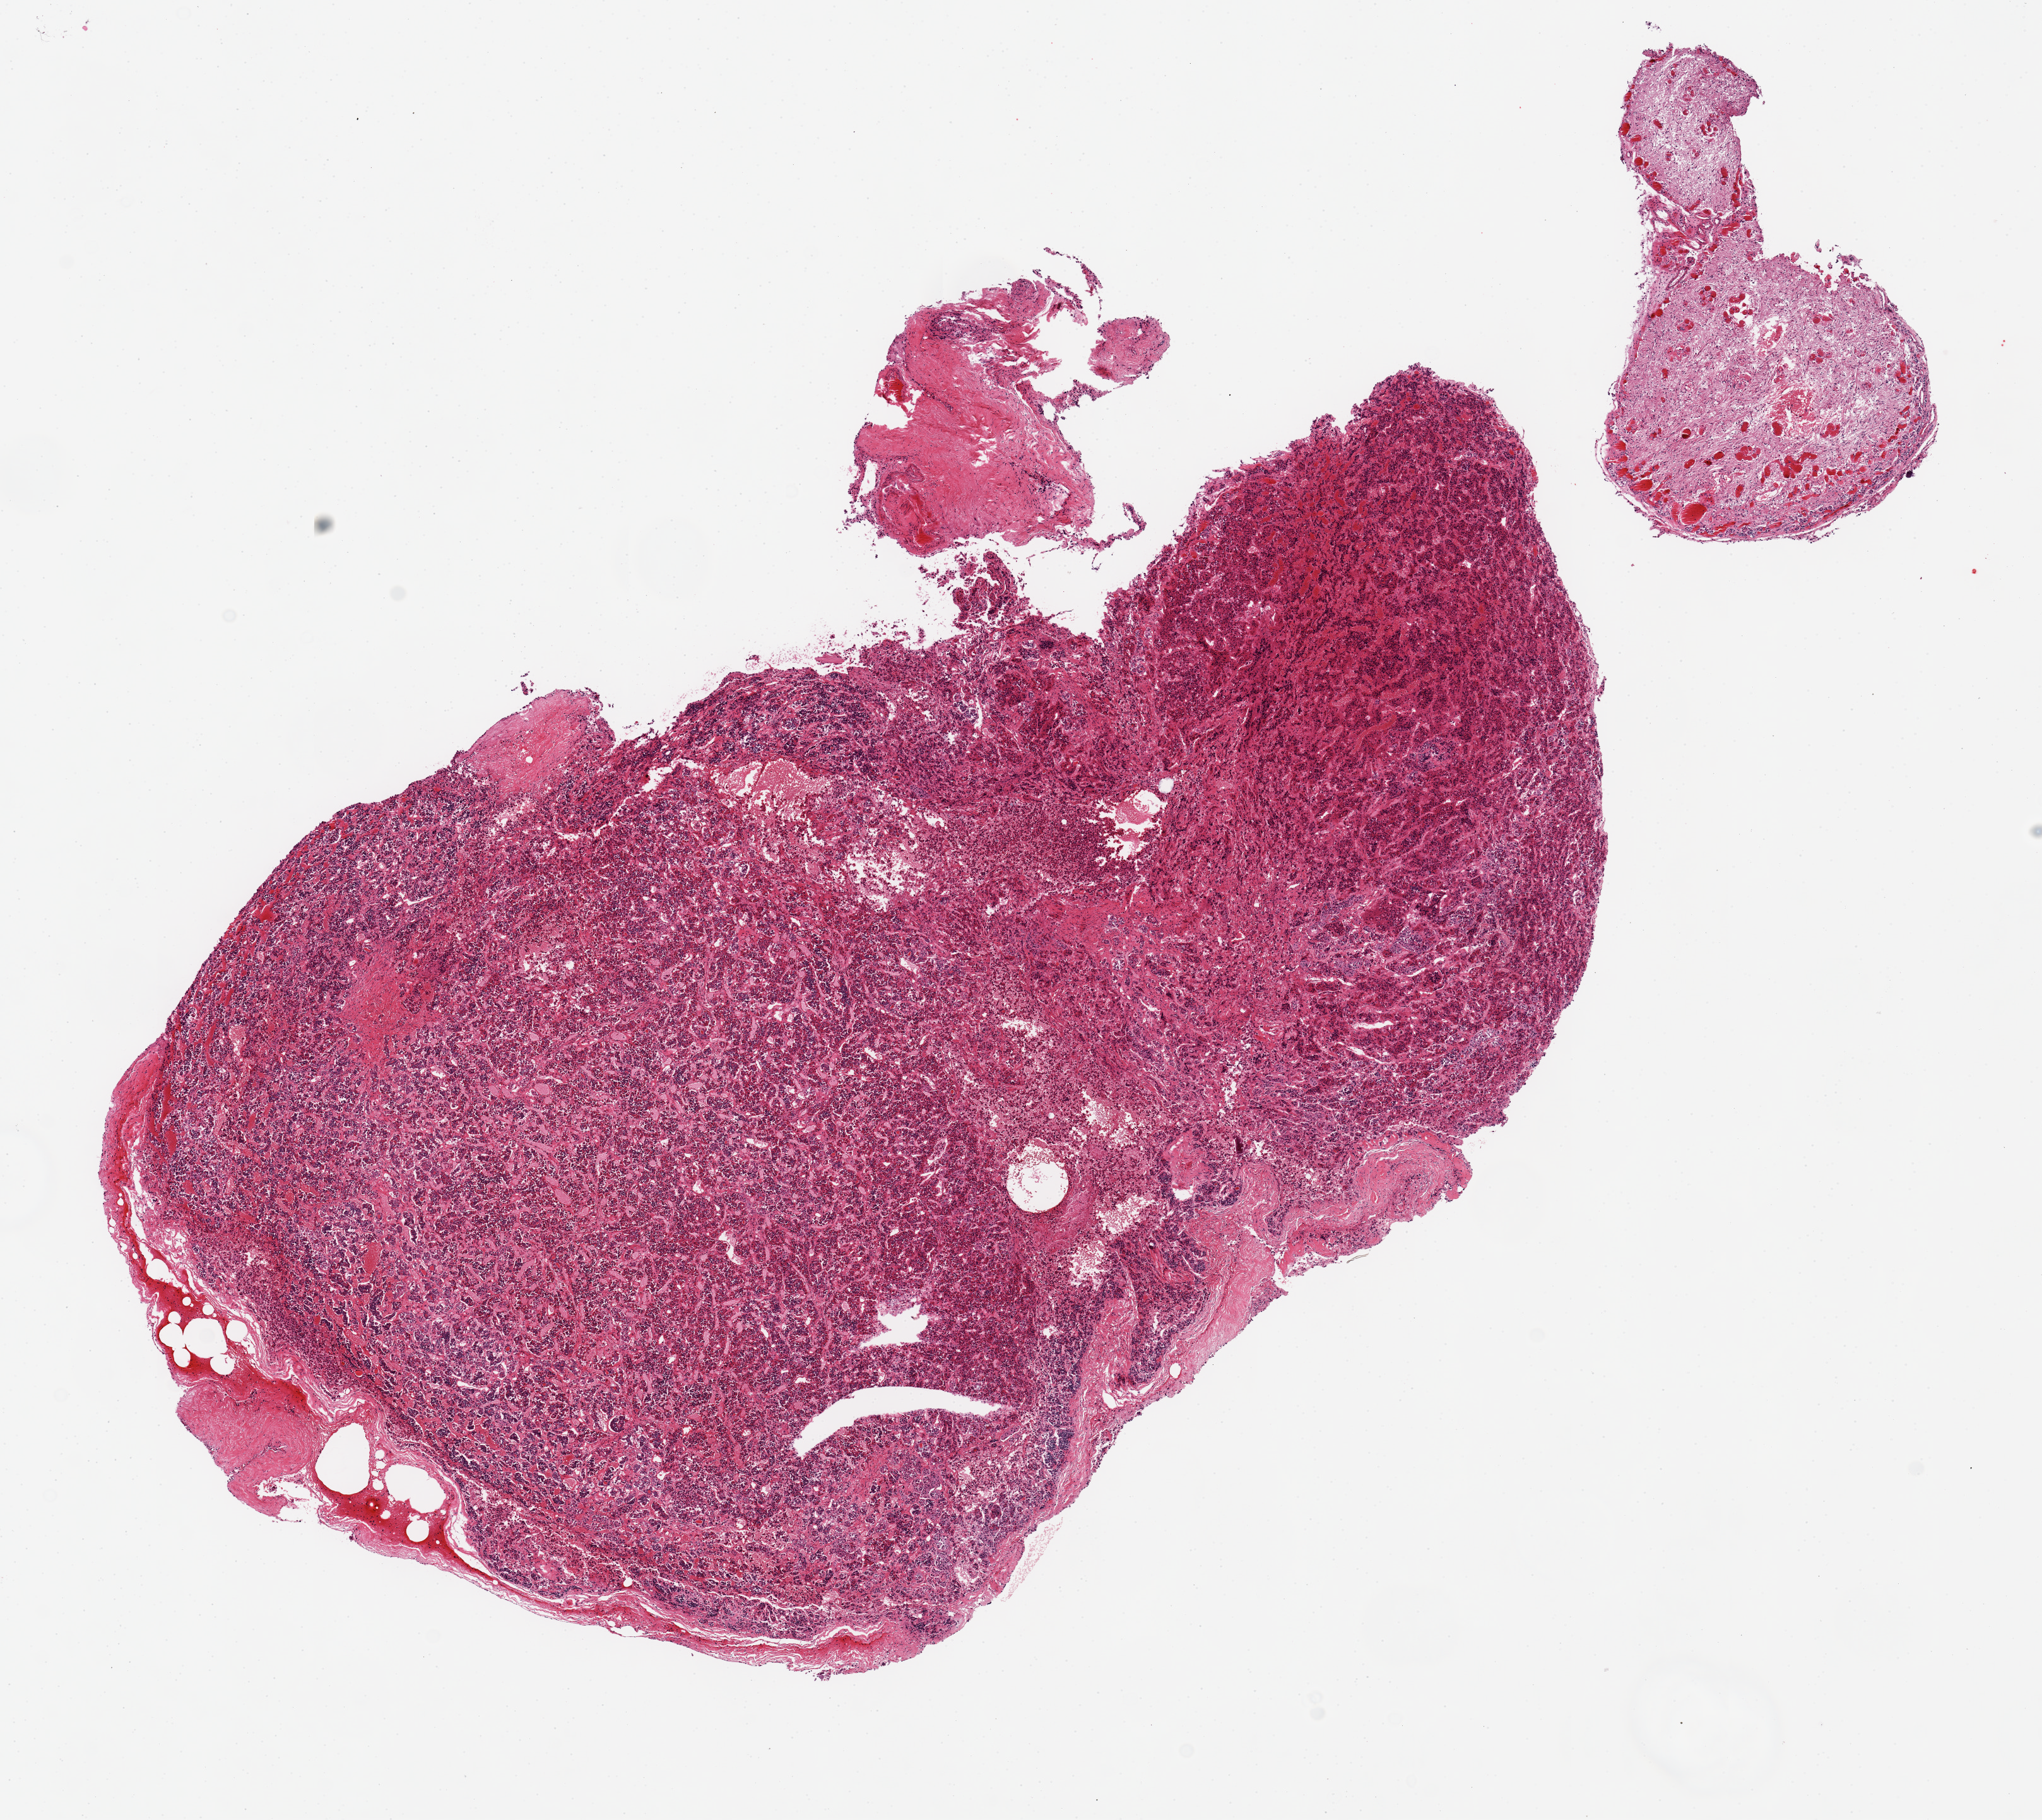
Digitized hematoxylin and eosin (H&E)-stained section — a low-resolution overview of the entire scanned area, about 12.8 x 11.4 mm (slide scanned at 20x), PAXgene-fixed, paraffin-embedded tissue, sampled site (target tissue): pituitary, donor tissue sample. Donor sex: female.
Pathologist's review note for this sample: 2 pieces, 10x6 (anterior), 3x2 mm (posterior).